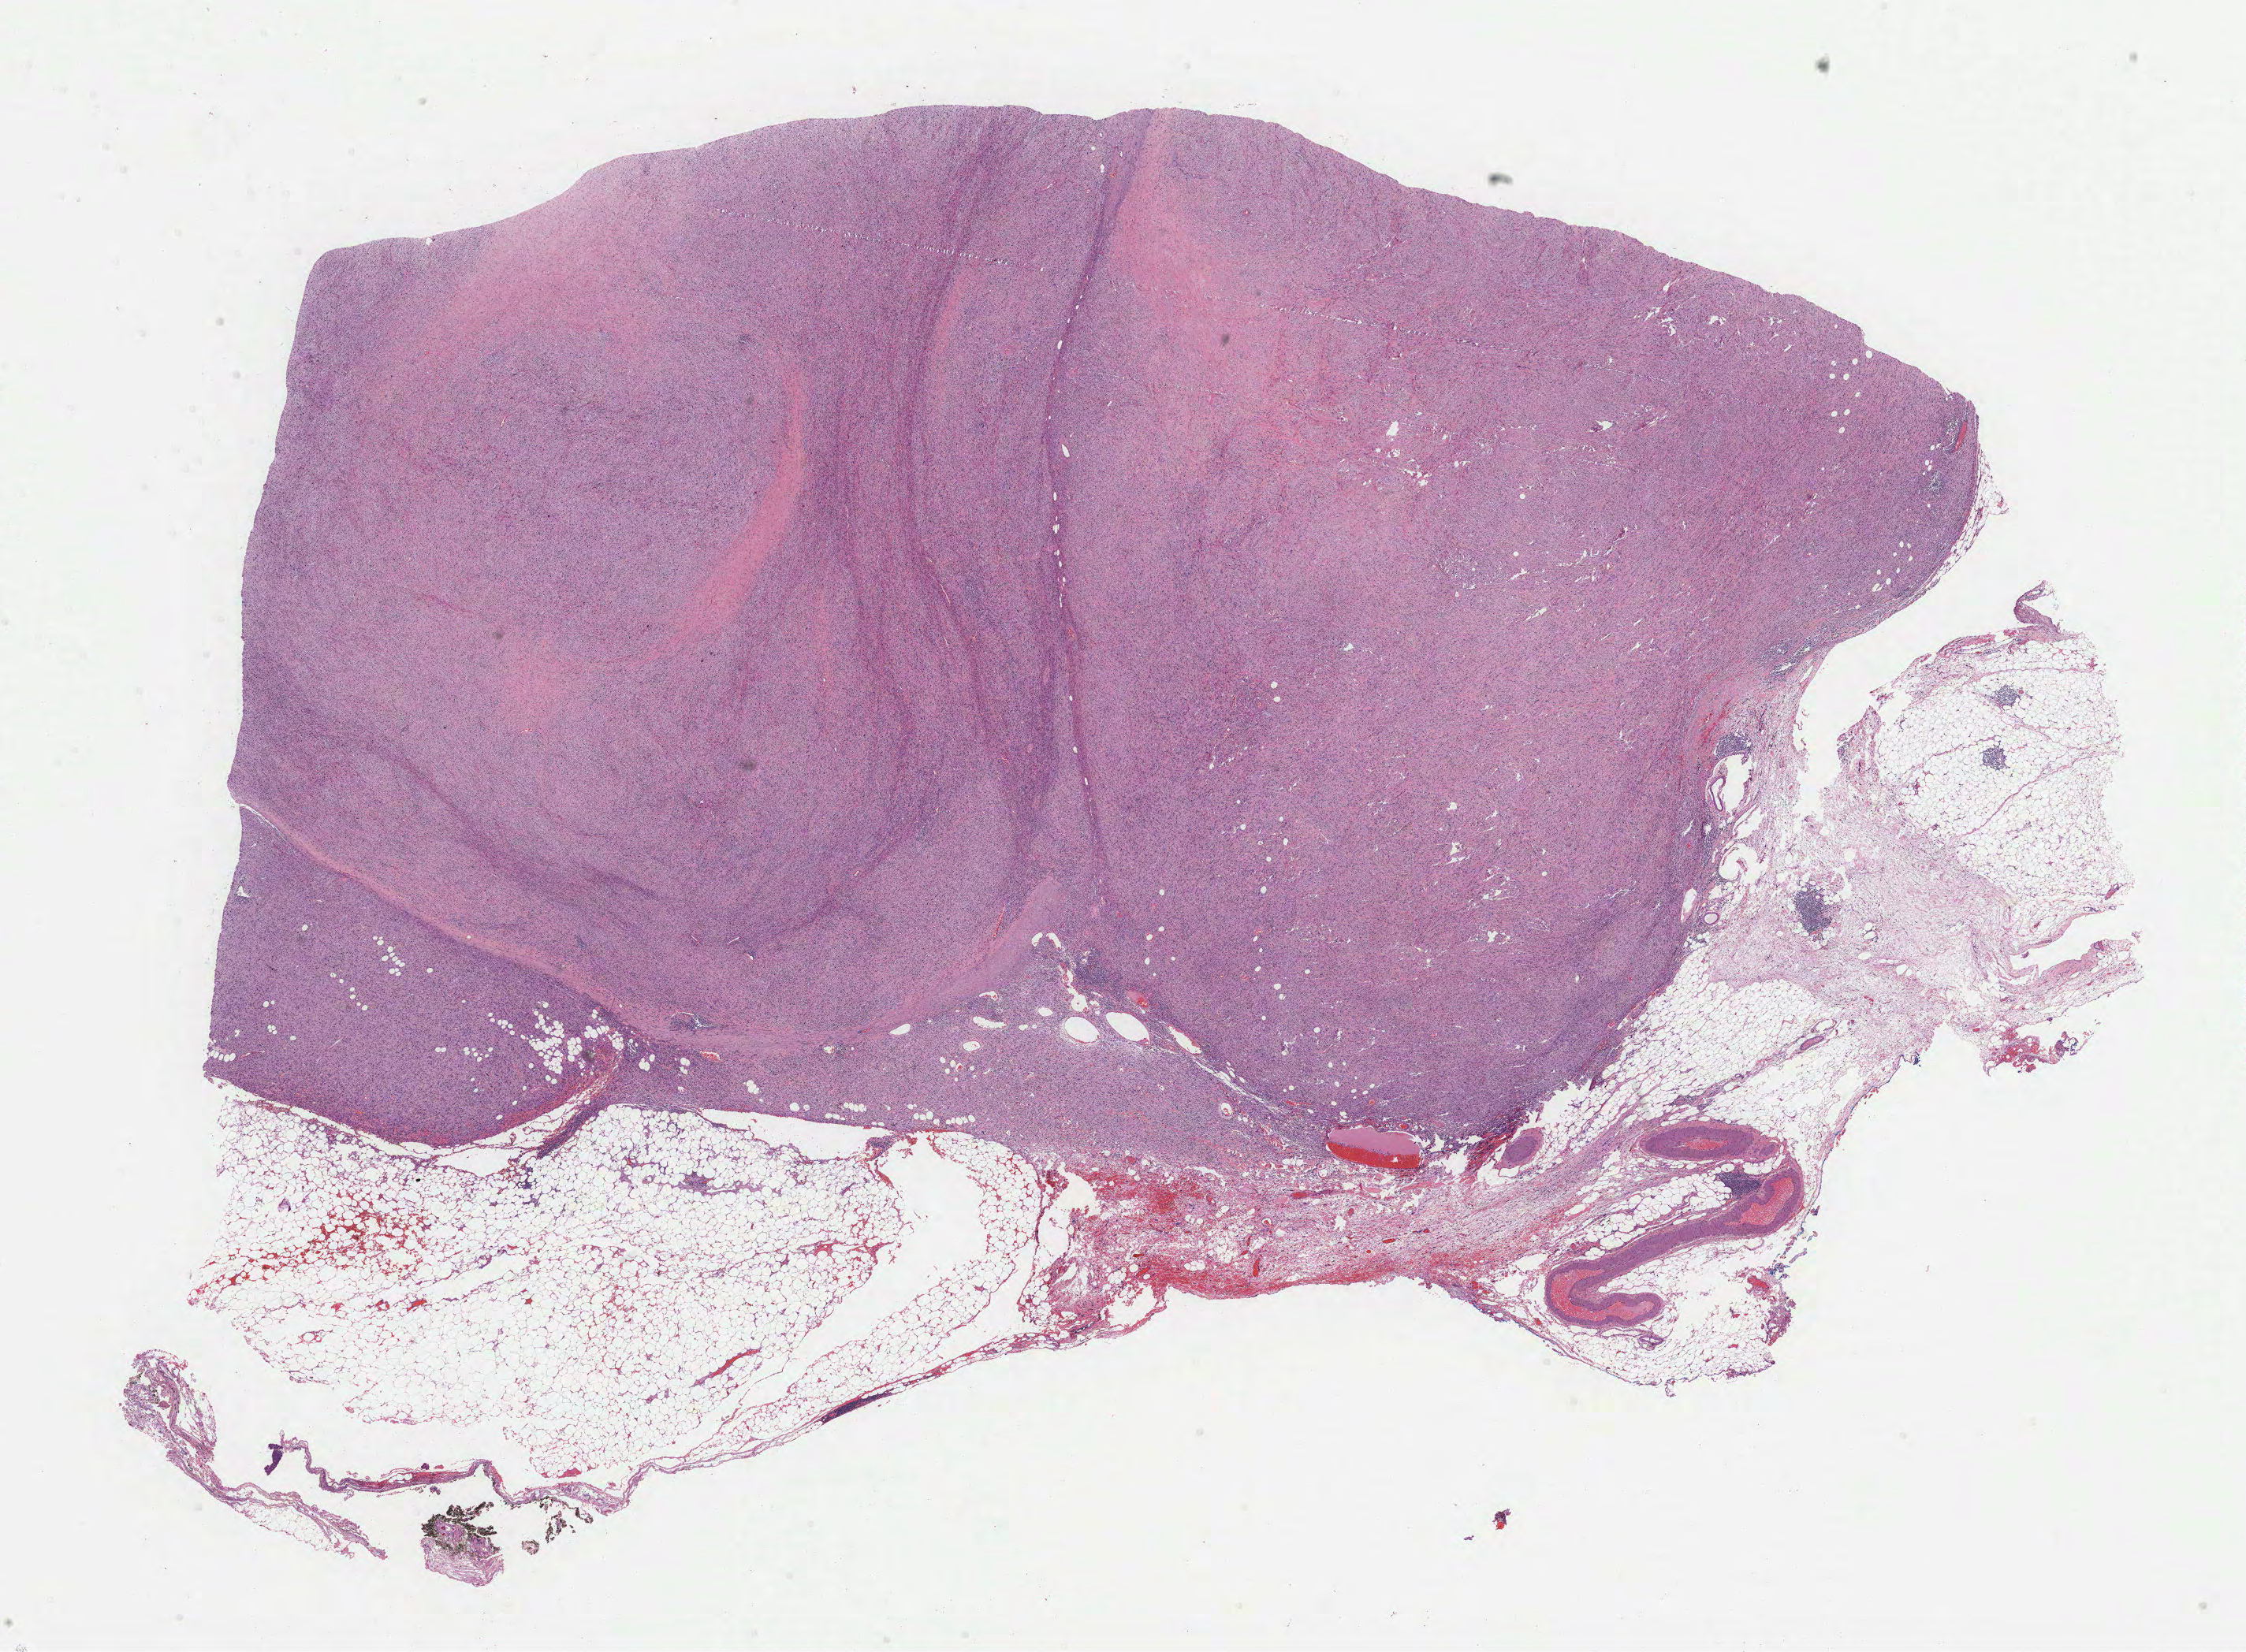
Digitized H&E-stained tissue section (whole slide) — a low-resolution overview of the entire scanned area, about 23.0 x 16.9 mm; formalin-fixed paraffin-embedded (FFPE) diagnostic section; primary tumour sample from the retroperitoneum and peritoneum. Male, age 75 years at initial diagnosis.
• pathologic diagnosis: Dedifferentiated liposarcoma (retroperitoneum)